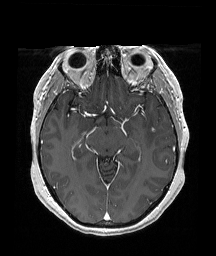
Brain MRI from a brain-tumour surgery series, one axial slice; position 113 of 192 along the scan axis; T1-weighted post-contrast; 1 mm slice thickness; 216 × 256 image matrix, field of view 211 × 250 mm. From the clinical record (not read from this slice): histopathology: Papillary glioneuronal tumor; WHO grade: 1.
Outlined on this slice (manually delineated by an expert):
- tumour: bounding box (x1, y1, x2, y2) in pixels: (151, 128, 154, 131)